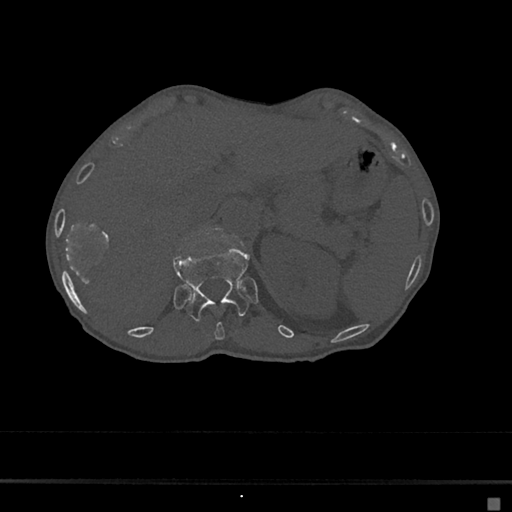
CT including the spine, one axial slice. Slice 128 of 797 in the series (ordered by position). Bone window (W 1800 / L 400 HU). 512 × 512 image matrix. Female patient, age 68 years. From the clinical record (not read from this slice): primary cancer: renal.
Annotated regions visible in this slice (semi-automatic segmentation, software-assisted and operator-edited):
- T11 vertebra: box from (x=215, y=321) to (x=225, y=341) px
- T12 vertebra: (x=173, y=247)–(x=249, y=322)